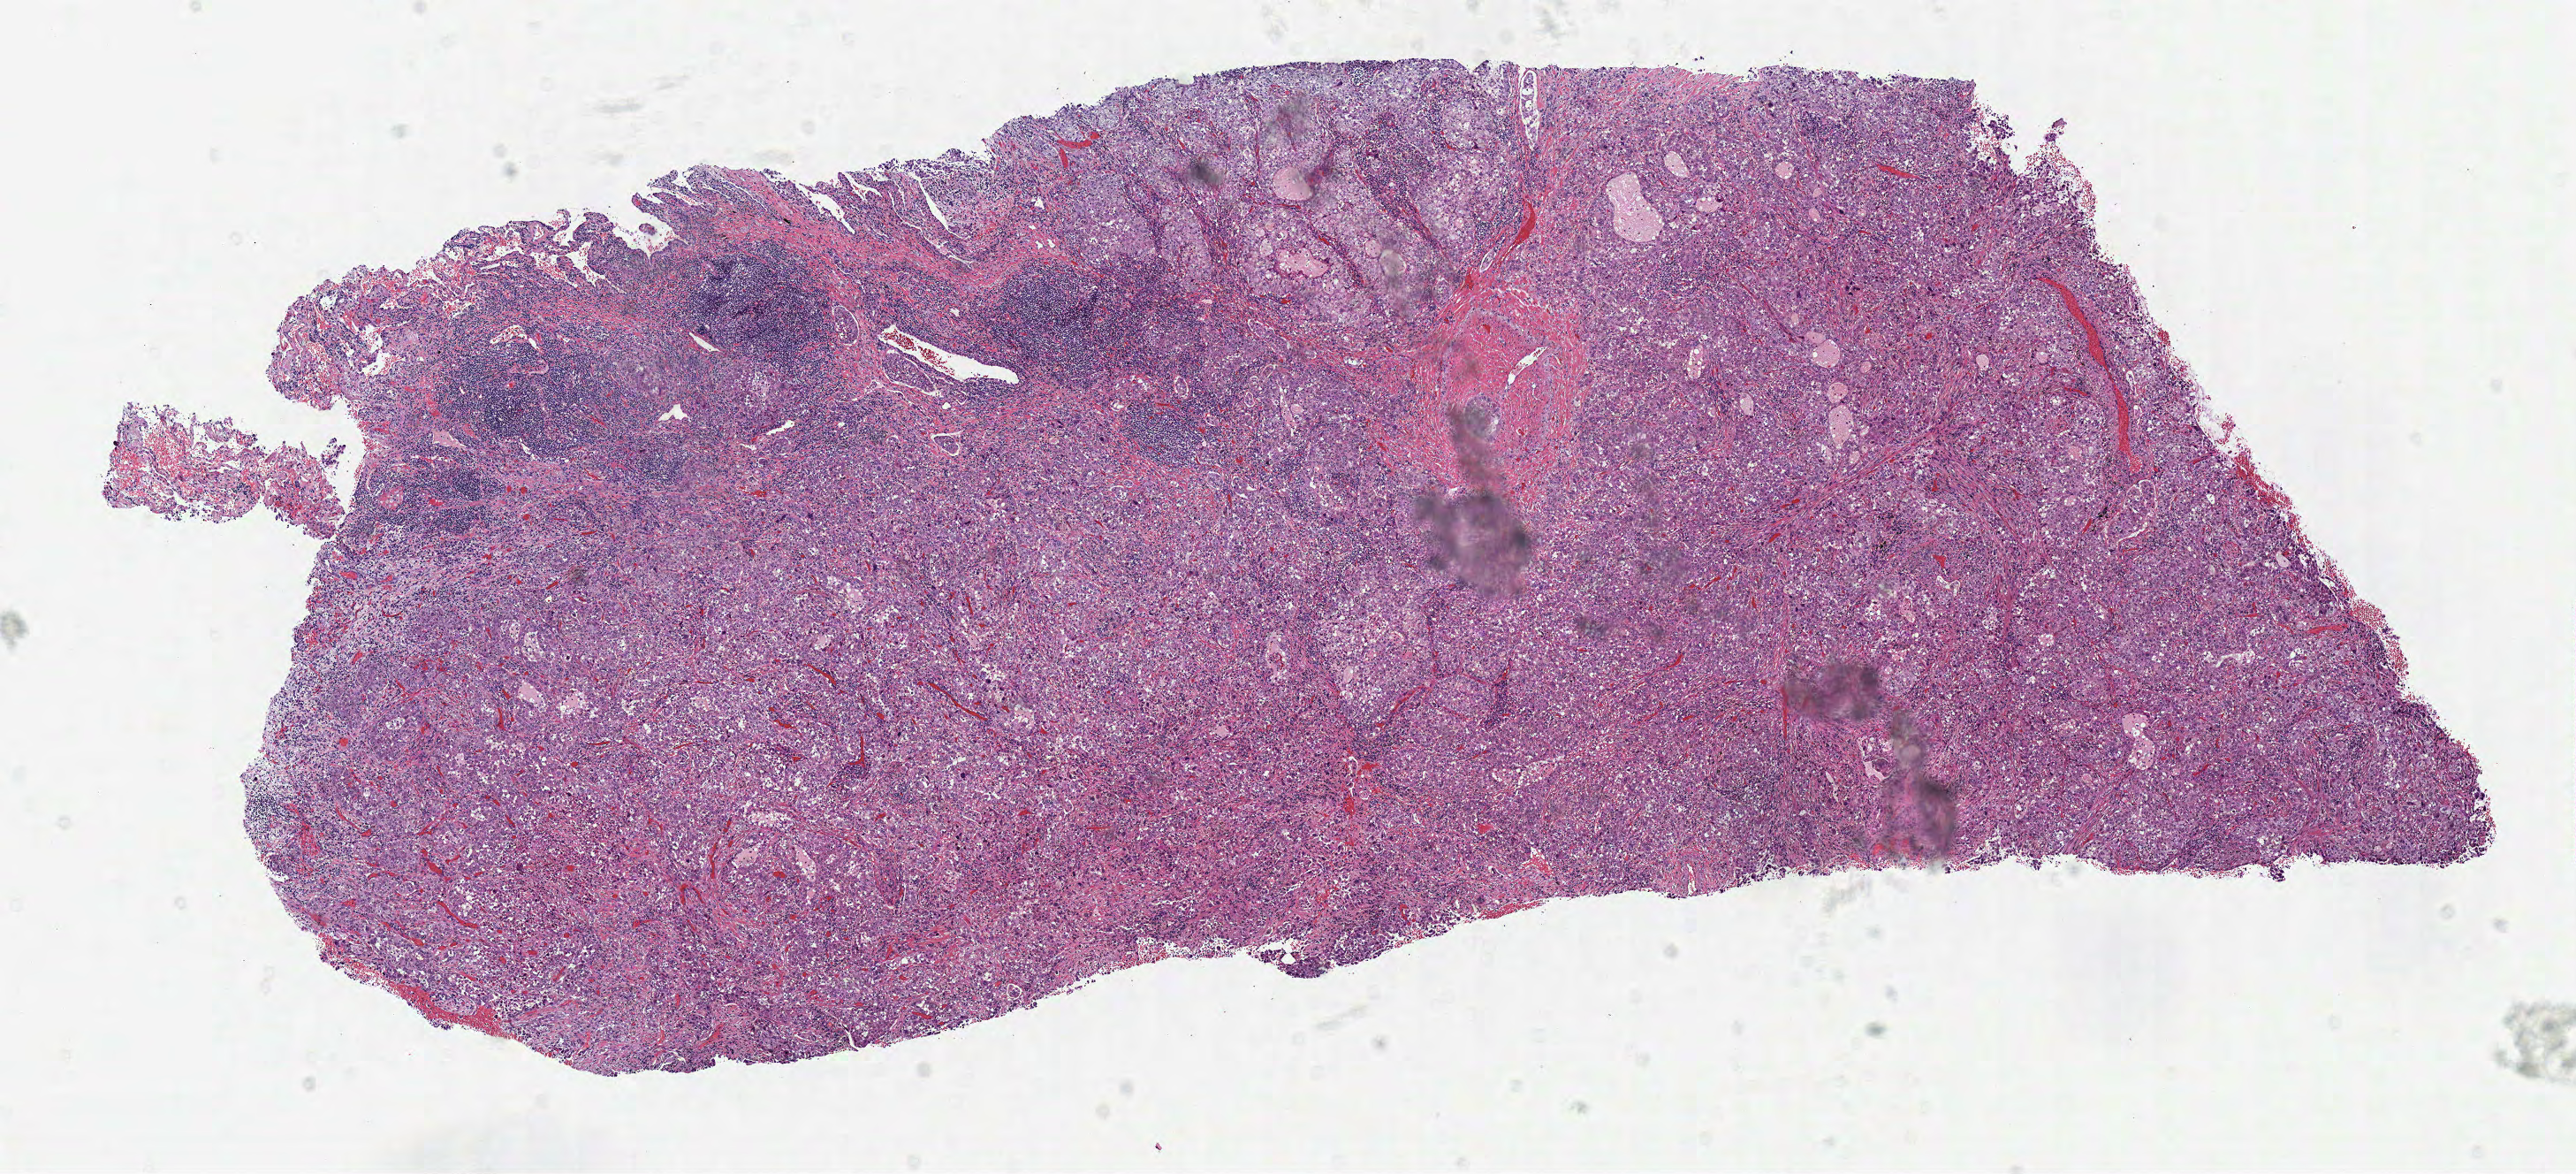
Whole-slide histology image, H&E — a low-resolution overview of the entire scanned area, about 11.5 x 5.2 mm (from a 40x scan), frozen section, primary tumour sample from the lung. Female, age 62 years at initial diagnosis. Composition of this section per pathologist review: tumour cells 95%, tumour nuclei 75%, normal cells 5%, stromal cells 0%, necrosis 0%. Inflammatory infiltration, as recorded: lymphocyte infiltration 15%, monocyte infiltration 0%, neutrophil infiltration 5%.
Laterality: right. Histologic diagnosis: Adenocarcinoma, NOS (upper lobe, lung). AJCC pathologic stage: IA (7th edition).